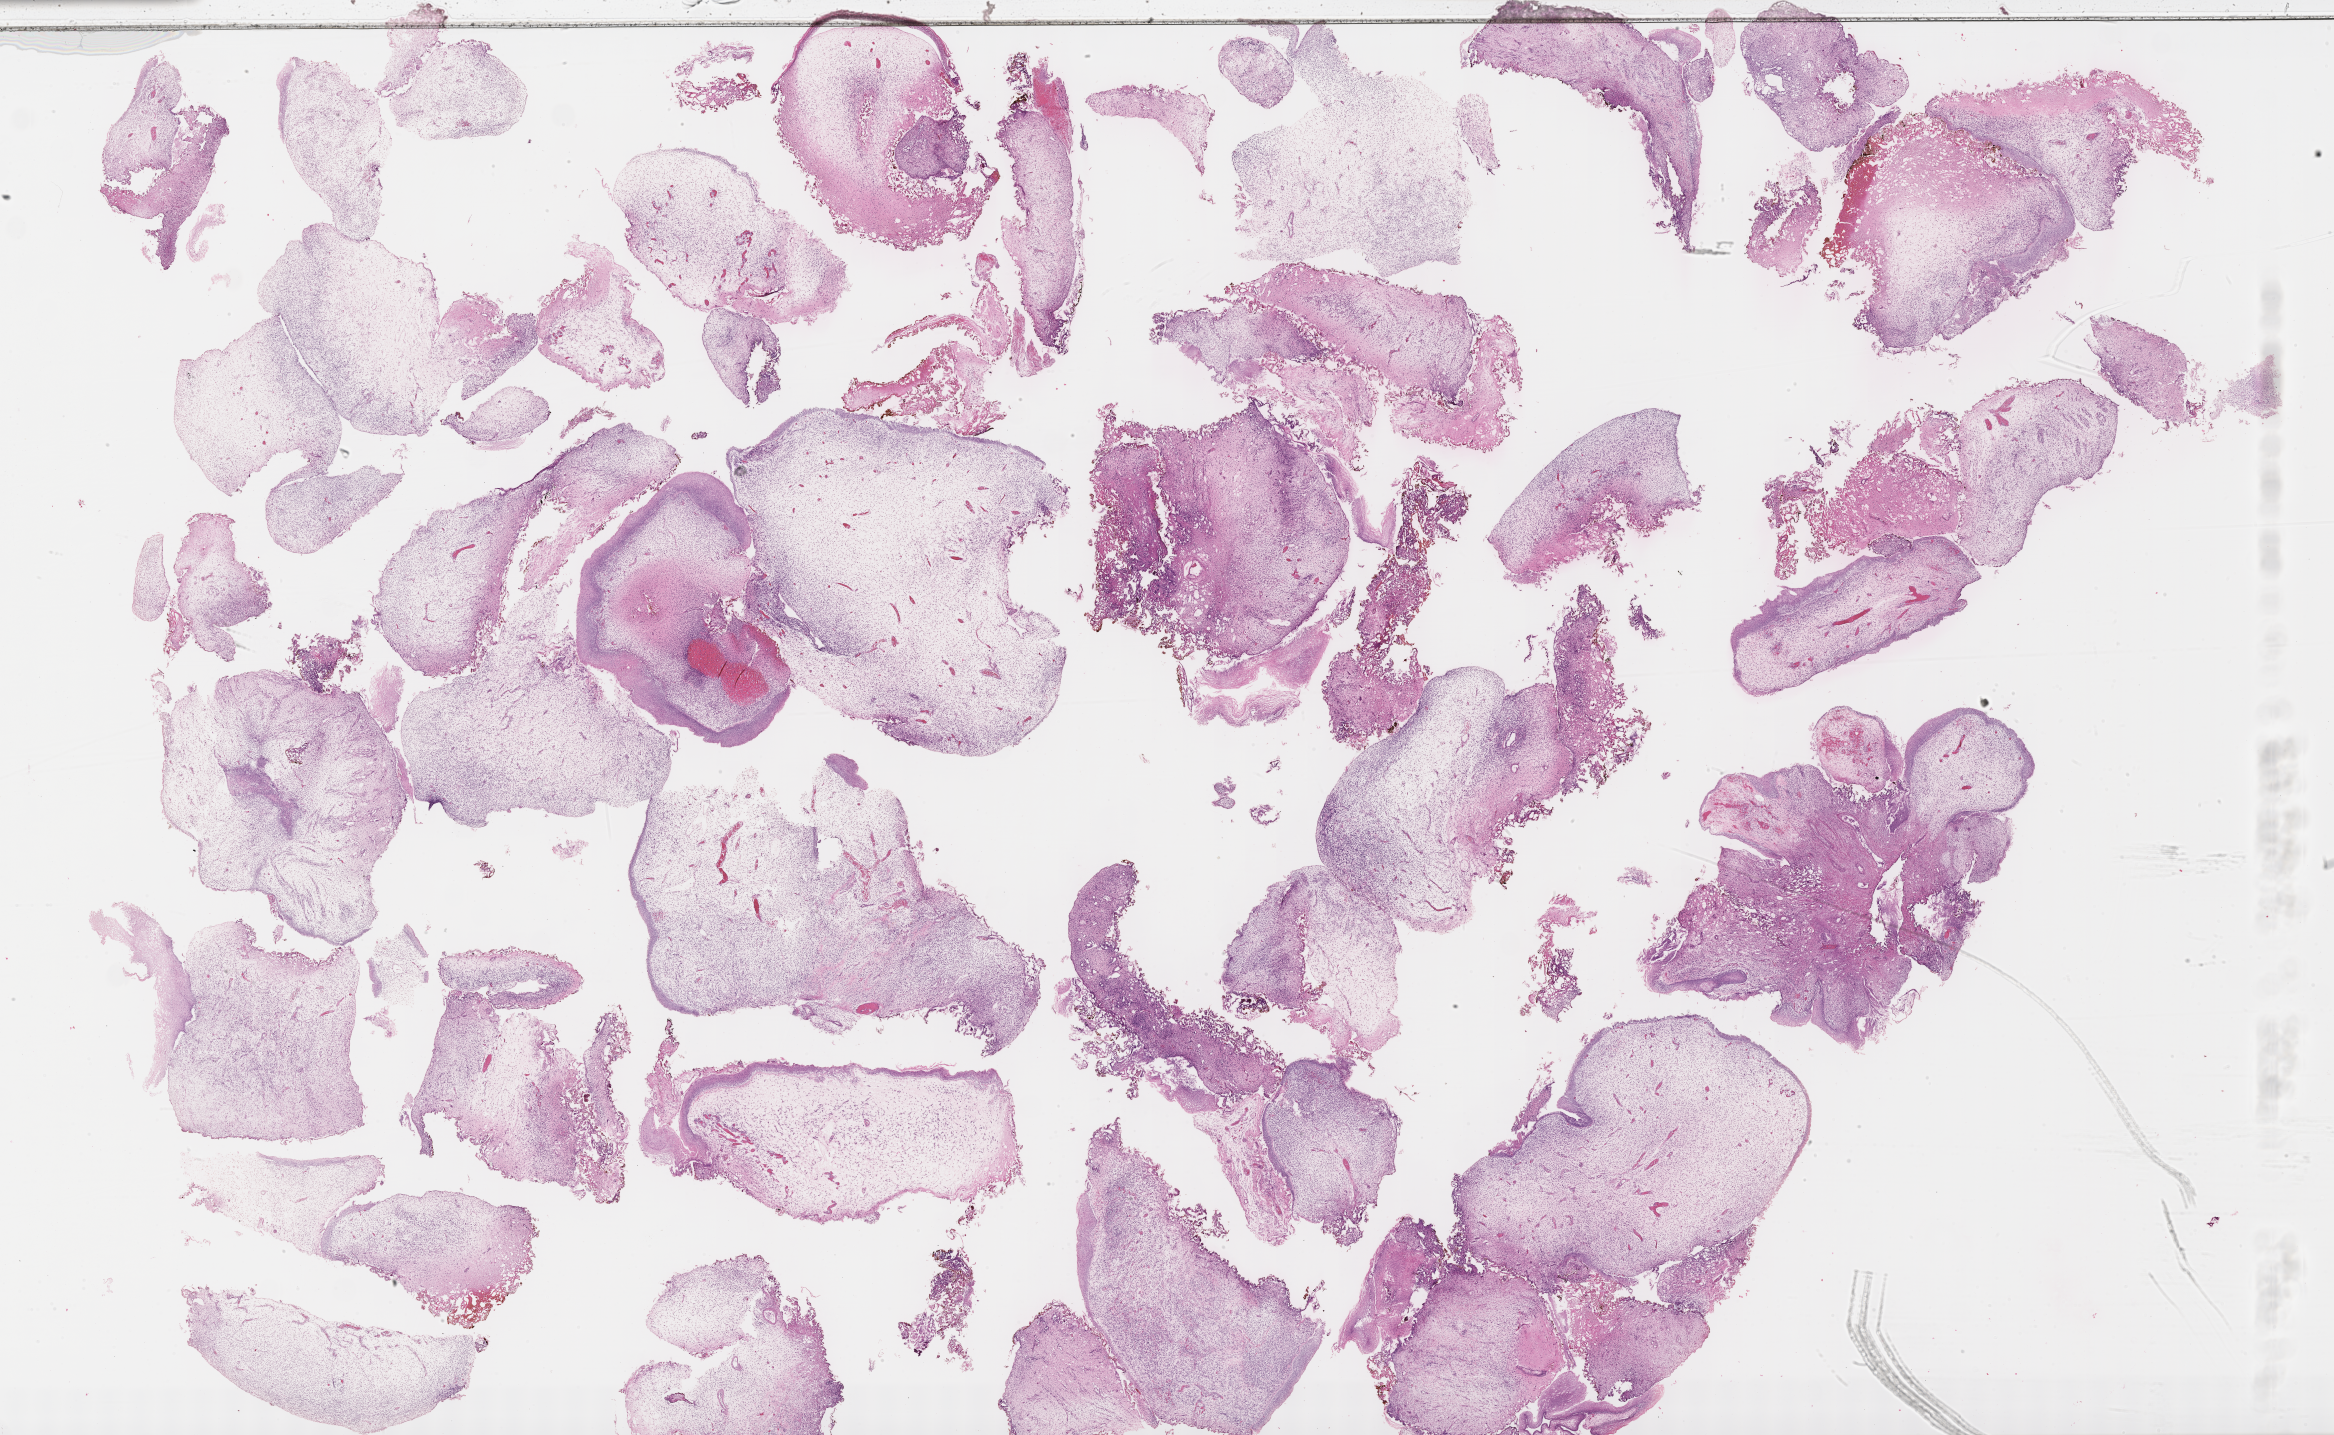
Haematoxylin and eosin whole-slide image of tumor tissue — a low-resolution overview of the entire scanned area, about 37.7 x 23.2 mm, formalin-fixed, paraffin-embedded (FFPE) tissue. Patient: male, age 14.5 years at diagnosis.
Diagnosis: rhabdomyosarcoma; histological classification: embryonal rhabdomyosarcoma. Metastatic status at presentation (as recorded): non-metastatic. Stage (as recorded): 3.